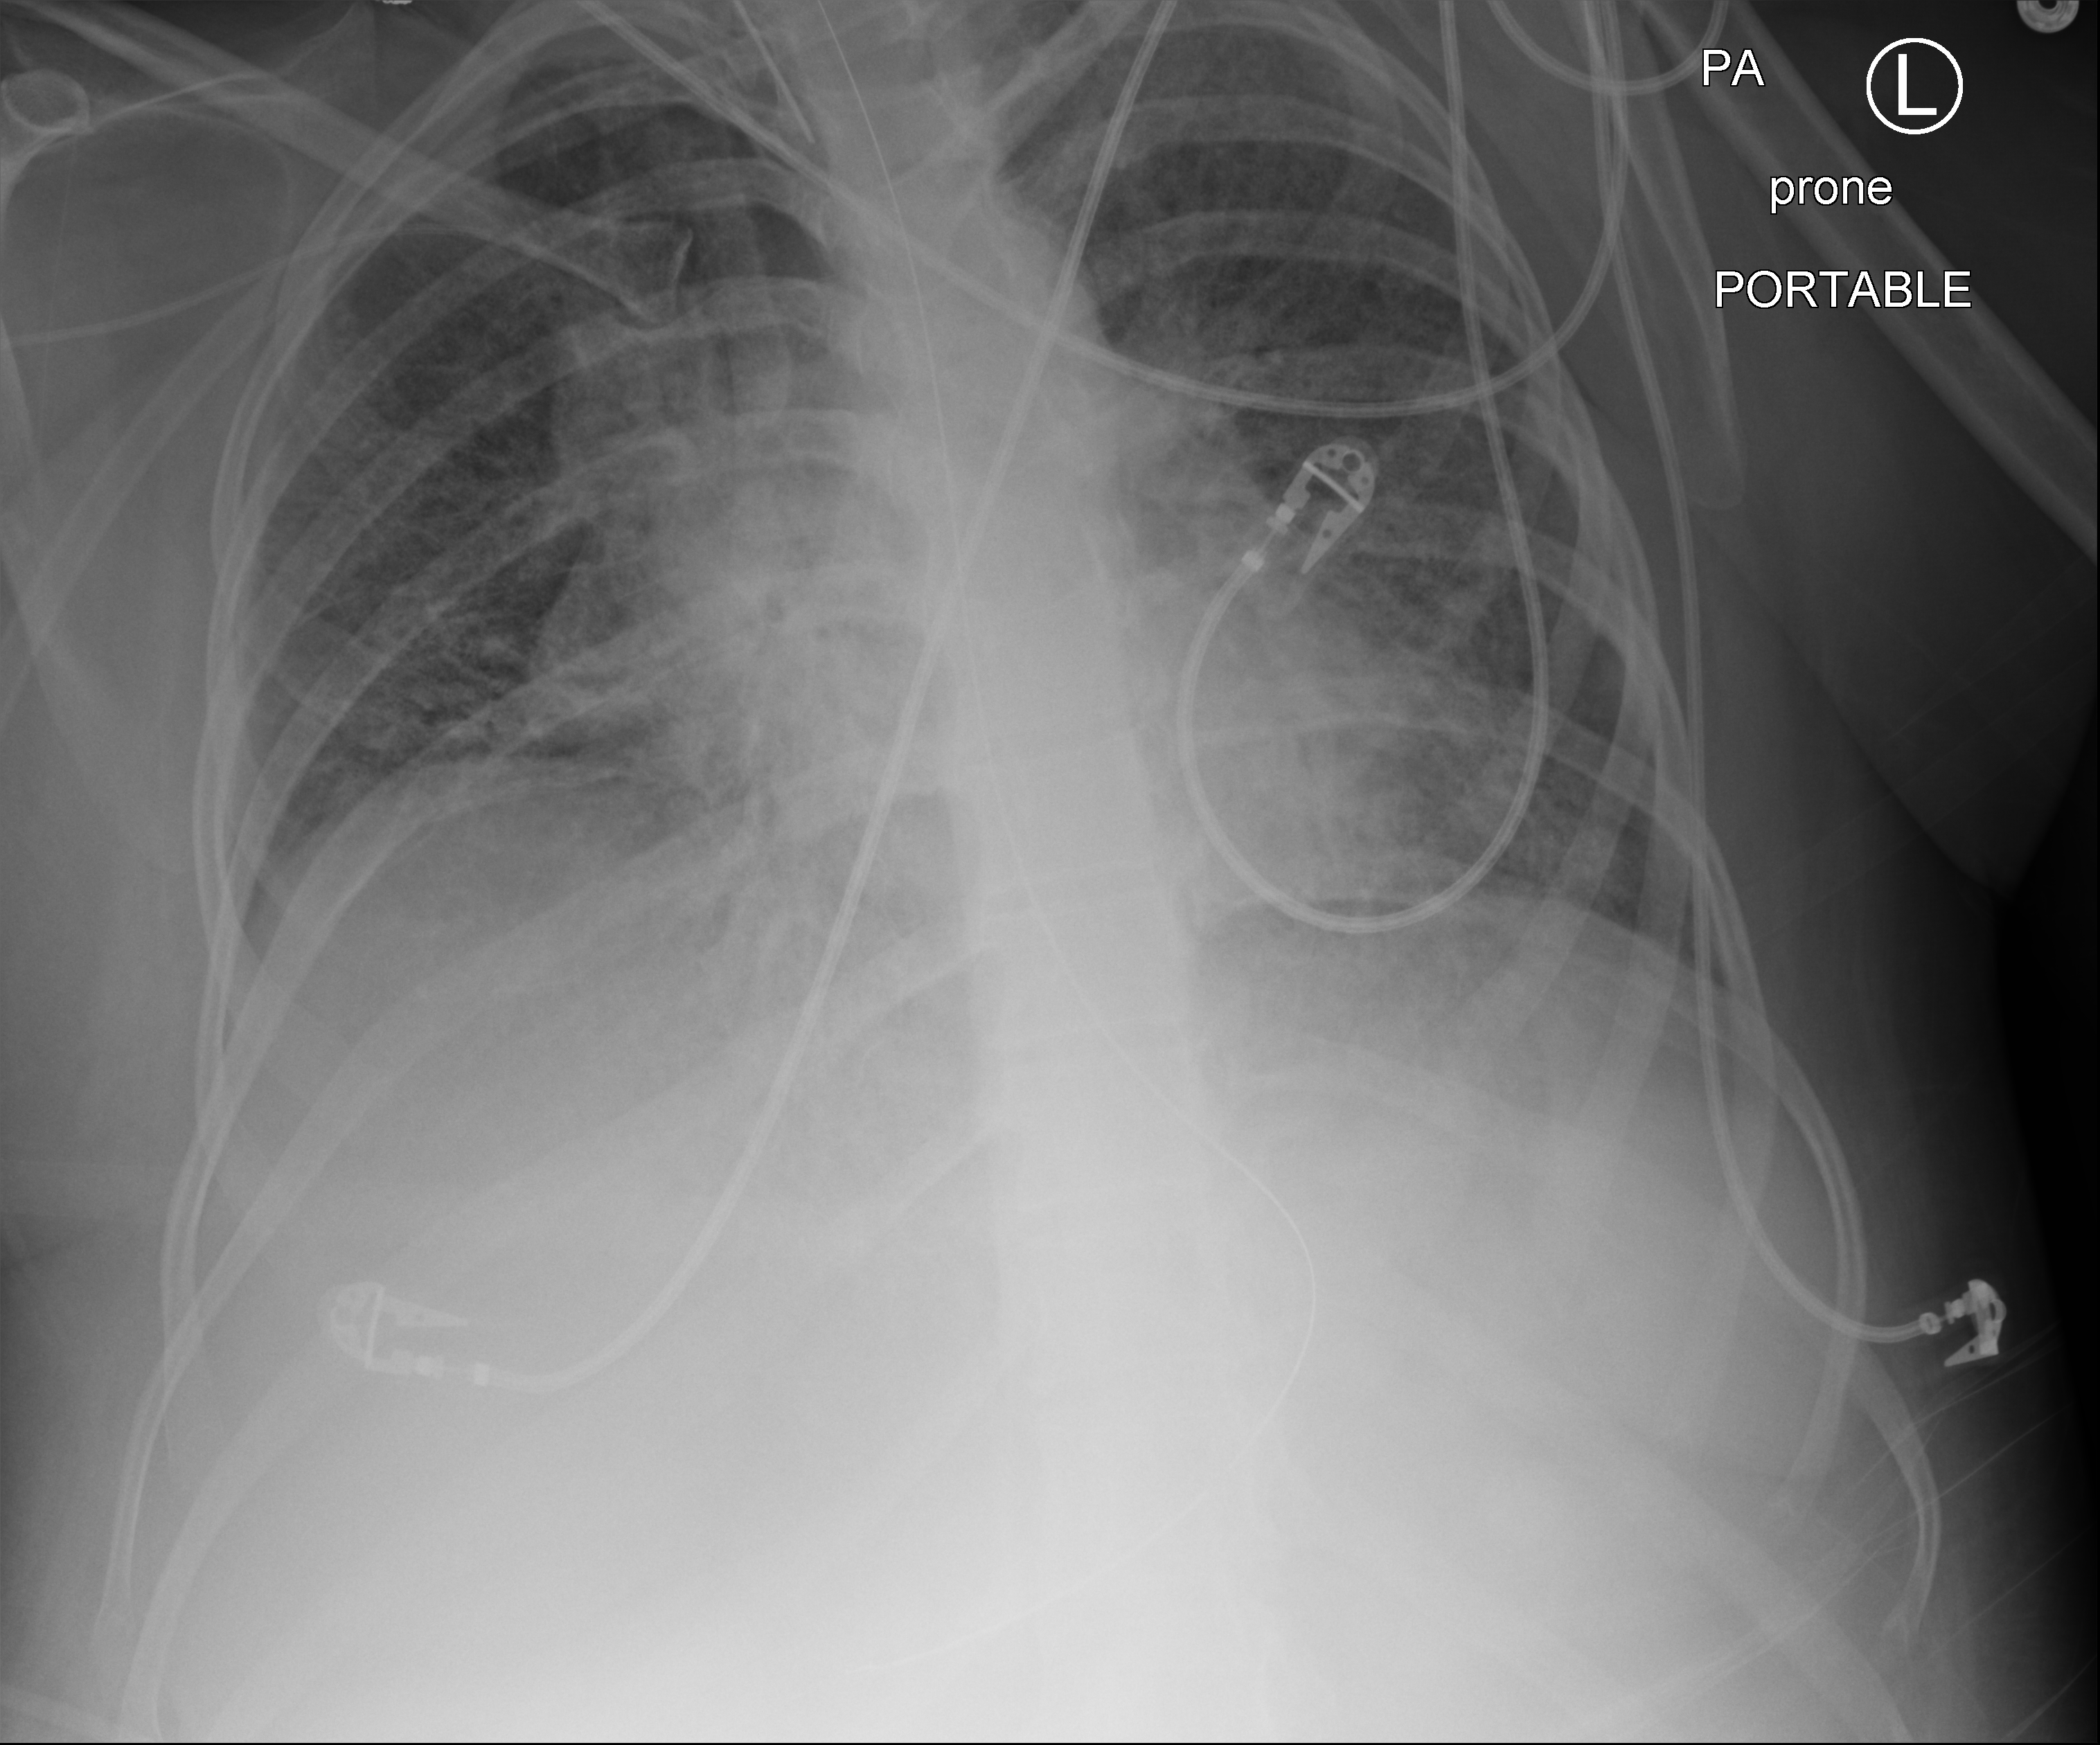
Chest X-ray (portable); posteroanterior (PA) projection. Female patient hospitalised with COVID-19, age 18–59 years.
Hospital-stay facts (about this admission, not read from this image; timing relative to this image not recorded):
- admitted to intensive care during this hospital stay: yes
- length of hospital stay: 73 days